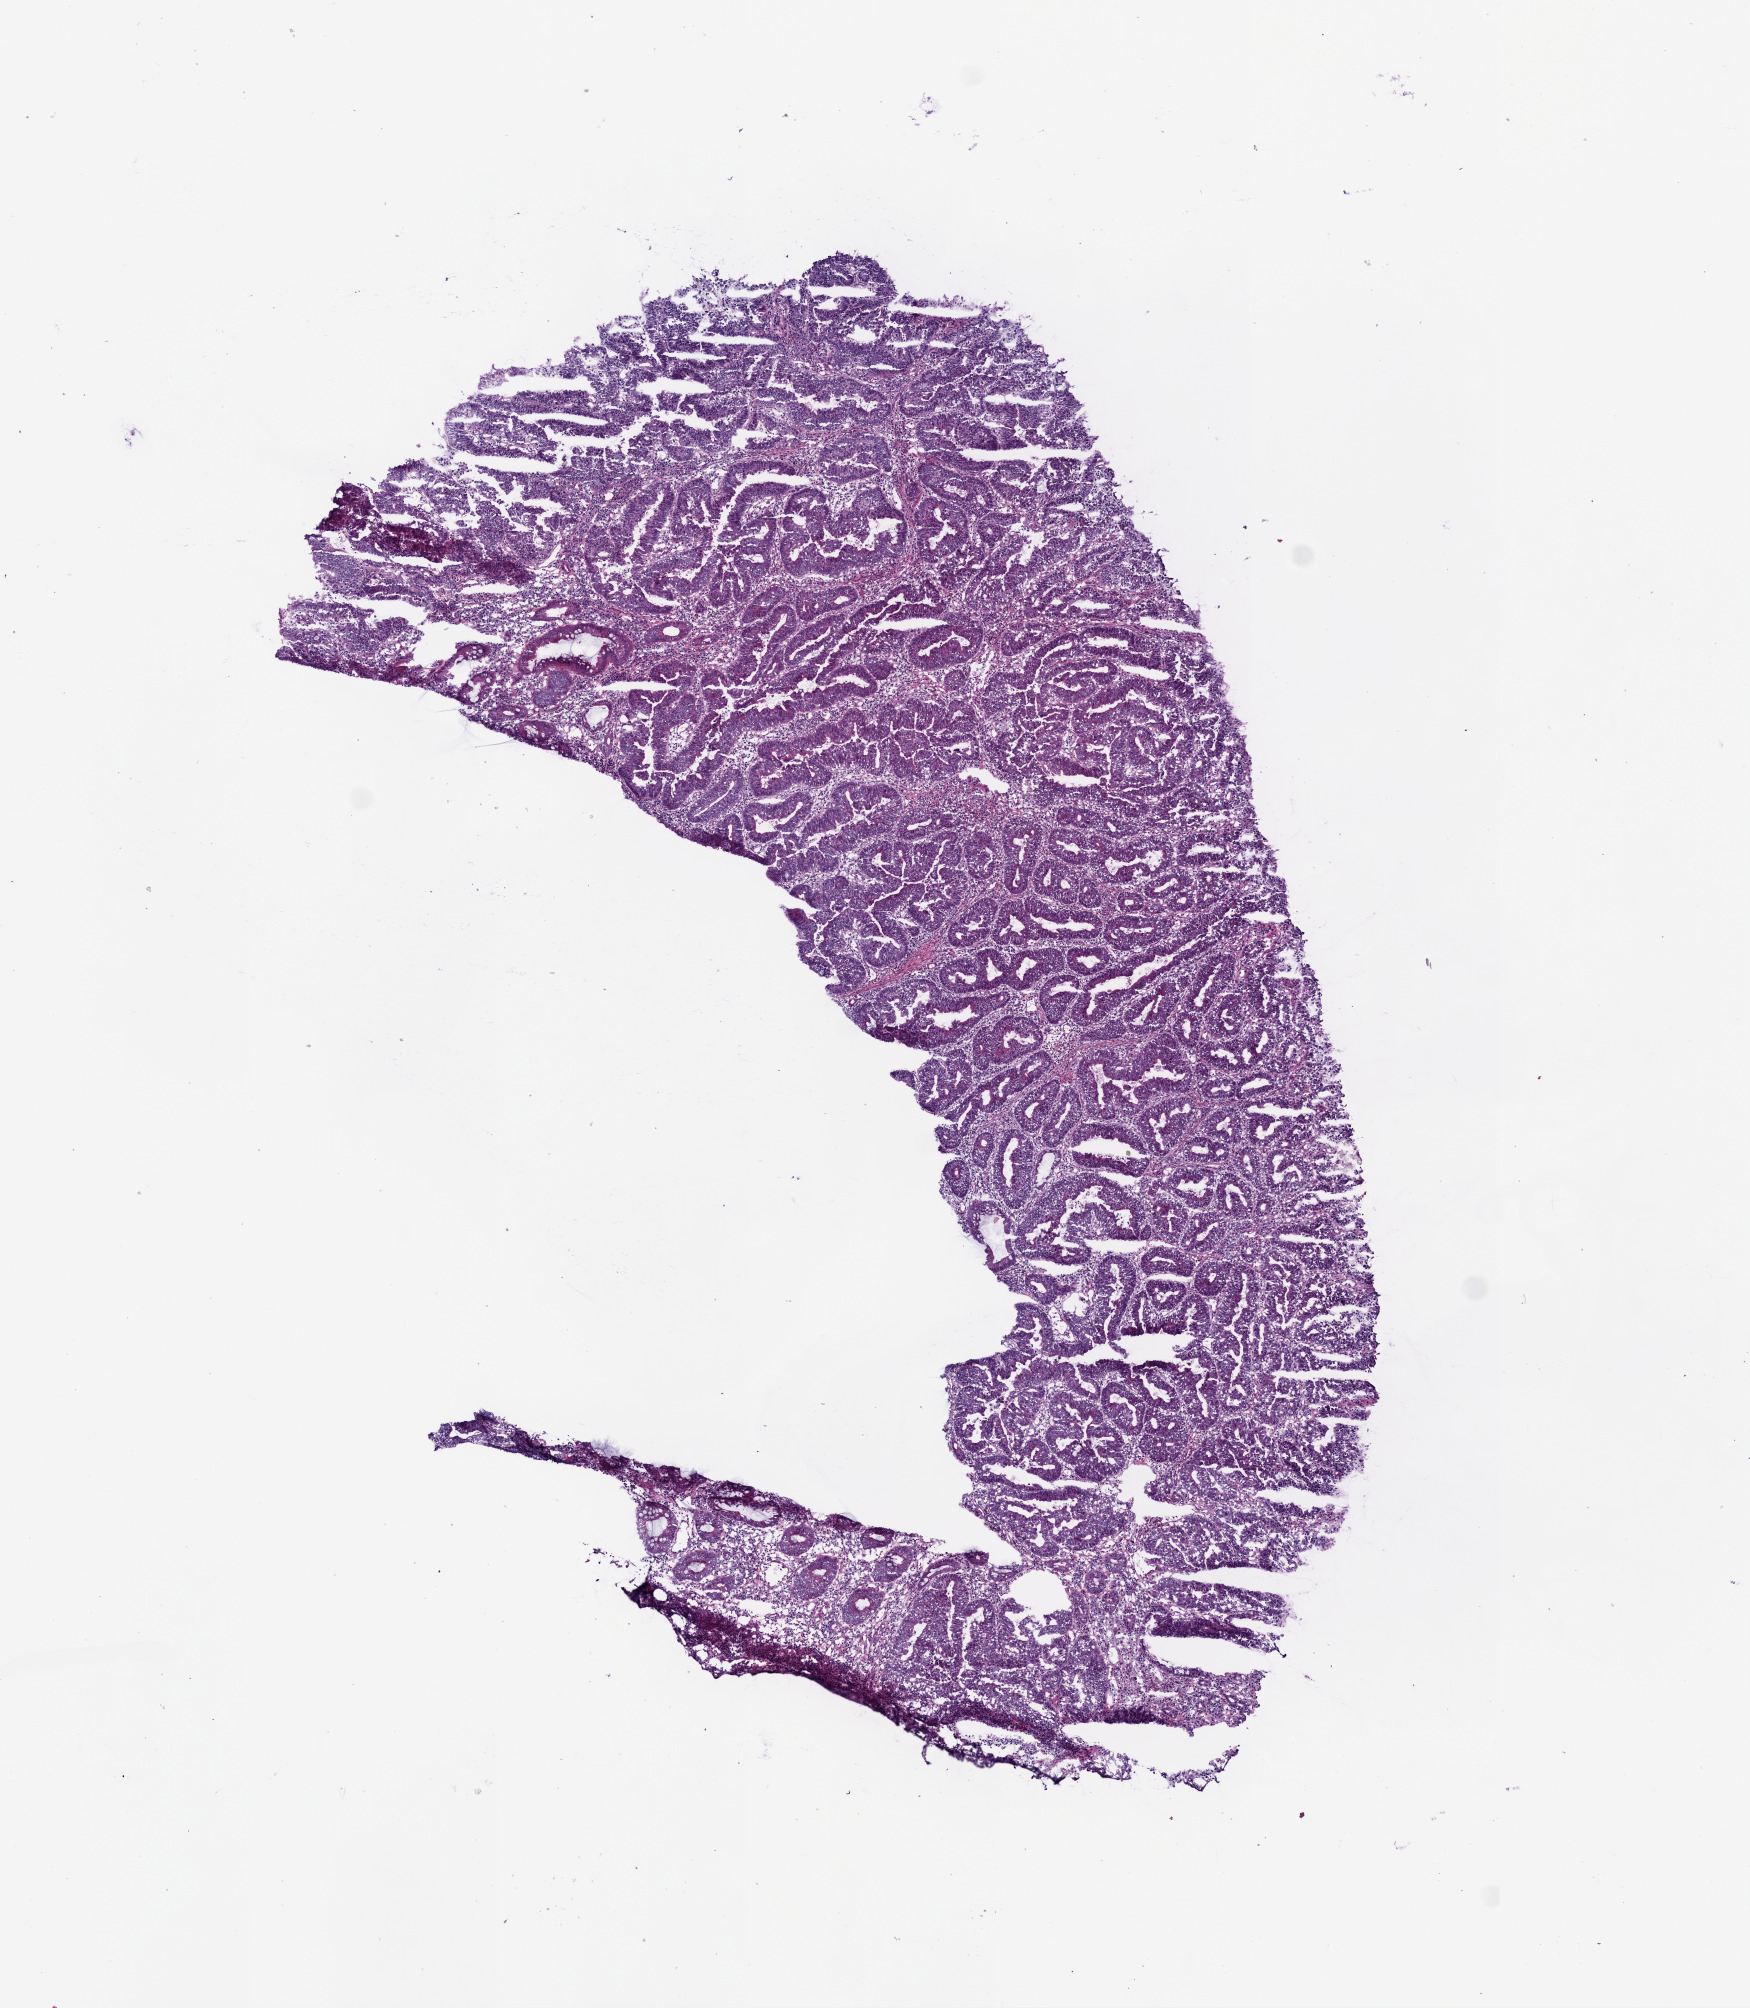
Whole-slide histology image, H&E-stained, low-resolution overview of the scanned area, about 7.0 x 8.1 mm; frozen section from the bottom of the tissue portion; primary tumour sample from the colon. Male, age 79 years at initial diagnosis. Slide review estimates, as recorded: tumour cells 85%, tumour nuclei 65%, normal cells 5%, stromal cells 10%, necrosis 0%.
• pathologic diagnosis: Adenocarcinoma, NOS (ascending colon)
• lymph nodes positive (case pathology): 0 of 18 examined
• AJCC pathologic stage: I (5th edition)